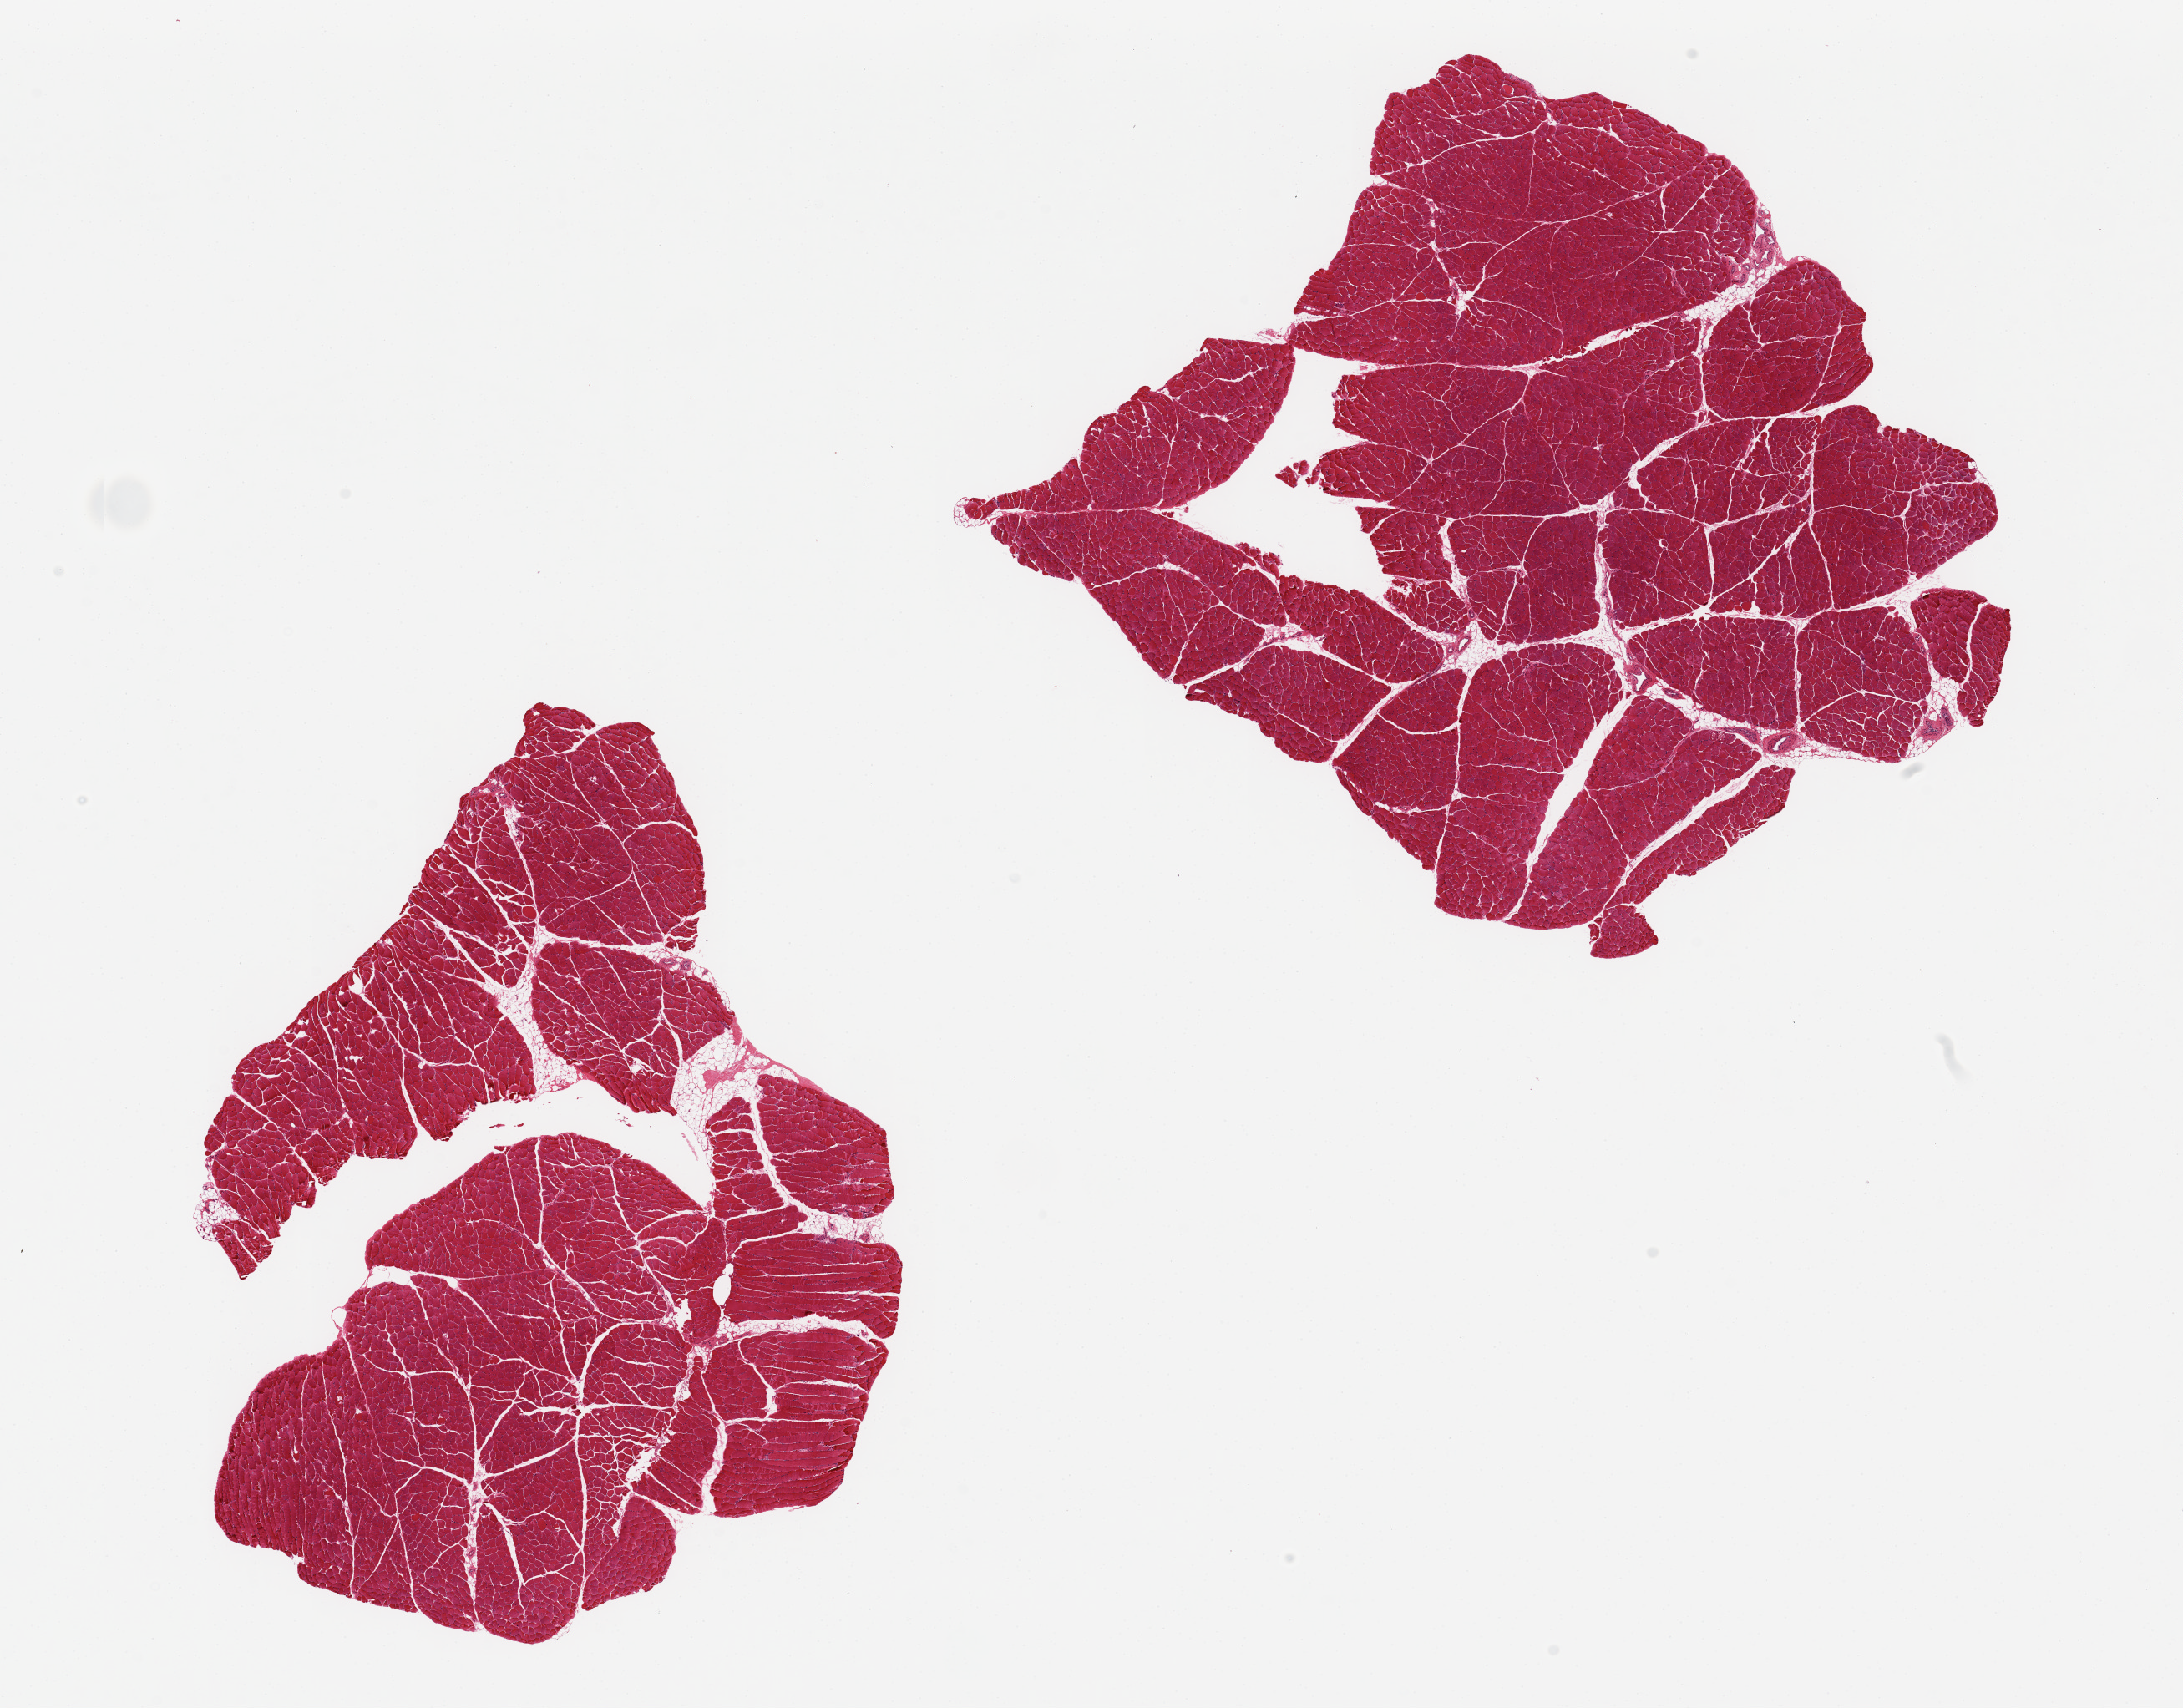
H&E whole-slide image, shown as a low-resolution overview of the whole scanned area (about 20.7 x 16.2 mm, acquisition: 20x scan); PAXgene-fixed, paraffin-embedded tissue; sampled site (target tissue): skeletal muscle; tissue donor sample. Donor: female.
Pathologist's review note for this sample: 2 aliquots, ~7x6mm. Minimal (<5%) interstitial fat.